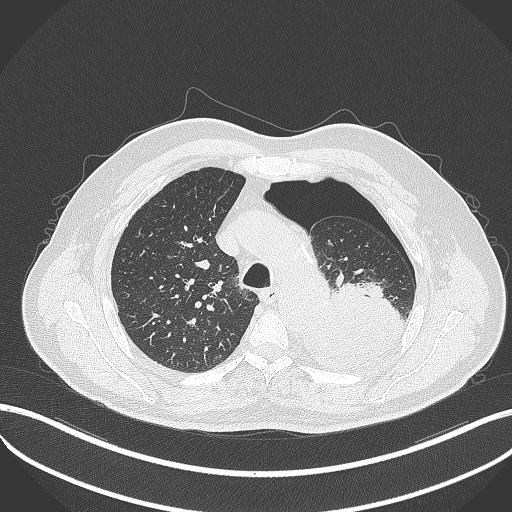
Chest CT, one axial slice. Slice 377 of 464 in the series (ordered by position). 120 kVp. Lung window (W 1500 / L -600 HU). 512 × 512 image matrix, field of view 400 × 400 mm. Patient: male, 76 years. Case-level facts recorded for this patient, not image findings: clinical TNM (as recorded): T3 N0 M1b.
Annotated regions visible in this slice (bounding box drawn by a radiologist):
- lung tumour (recorded histology: adenocarcinoma): bounding box (x1, y1, x2, y2) in pixels: (294, 274, 408, 375)